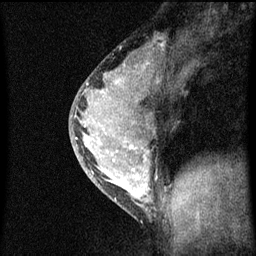
Breast MRI (dynamic contrast-enhanced), one sagittal slice. Position 36 of 60 along the scan axis. Dynamic contrast-enhanced series, image 2 of 3 at this slice position (ordered by acquisition). 1.5 T. TE 4.2 ms, TR 8 ms. 2 mm slice thickness. 256 × 256 image matrix. Patient: female, 33 years.
Structures marked on this image (semi-automatically segmented with operator editing):
- analysis volume of interest (the breast-tissue region the enhancement analysis was run in; not a lesion): bounding box <69,56,166,213> (left, top, right, bottom; pixels)
- tumour enhancement mask (voxels above the 70 % enhancement threshold inside the analysis volume of interest): <77,62,151,203>